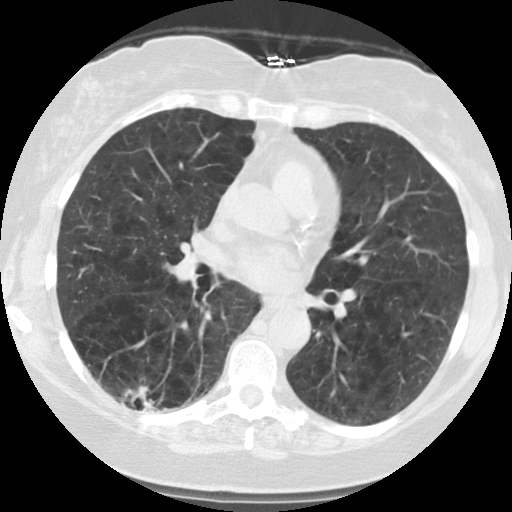
Low-dose screening chest CT, one axial slice. Position 59 of 122 along the scan axis. Reconstruction kernel STANDARD. Lung window (W 1500 / L -600 HU). 2.5 mm slice thickness. 512 × 512 image matrix, field of view 310 × 310 mm.
Structures marked on this image (outlined manually by an expert reader):
- lesion 1 (tumor, lower lobe of right lung): box from (x=124, y=386) to (x=160, y=409) px